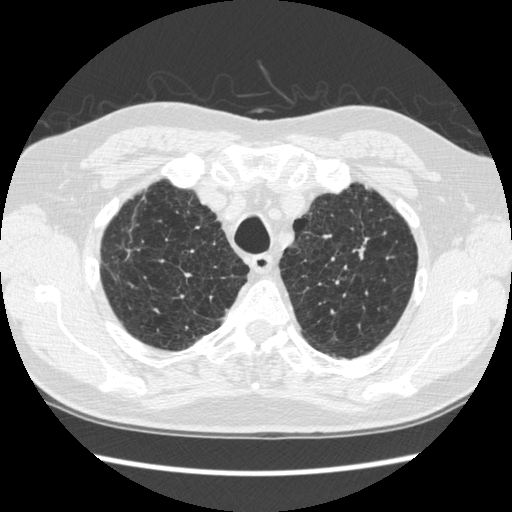
Chest CT (low-dose screening protocol), one axial image. Second annual screen. Lung window (W 1500 / L -600 HU). Standard (soft-tissue) reconstruction kernel (STANDARD). Slice 52 of 295 in the series. Male, age 70 years at enrolment. Former smoker at enrolment.
Expert reader's lesion annotation, bounding box <334,213,395,280> (left, top, right, bottom; pixels). The screening reader recorded 5 non-calcified nodules or masses ≥4 mm on this exam (right lower lobe, right lower lobe, right lower lobe, left upper lobe, left lower lobe); which of them this box marks is not recorded. Official screen result: positive, change unspecified: nodule(s) >= 4 mm or enlarging nodule(s), mass(es), or other non-specific abnormalities suspicious for lung cancer.